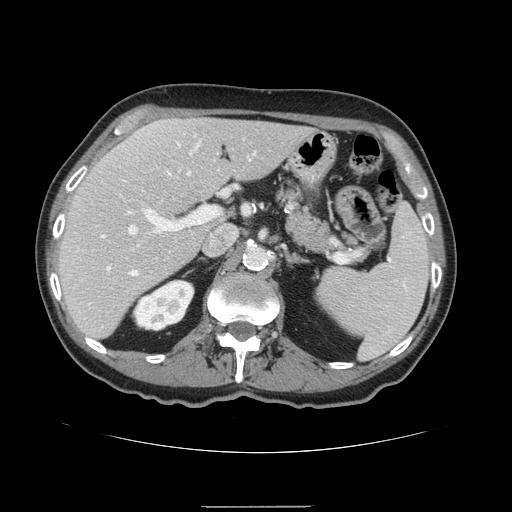
Contrast-enhanced abdominal CT, one axial slice; position 92 of 168 along the scan axis; soft-tissue window (W 400 / L 40 HU); 2.5 mm slice thickness; 512 × 512 image matrix. Male patient, age 74 years. From the clinical record (not read from this slice): diagnosis: colorectal cancer liver metastases, imaged before liver resection; multiple liver metastases: no; largest metastasis: 14.5 cm; chemotherapy before resection: no.
Outlined on this slice (outlined manually by an expert reader):
- hepatic veins: bounding box <128,158,251,274> (left, top, right, bottom; pixels)
- liver: <58,119,313,339>
- planned liver remnant (the part of the liver to remain after resection): <58,119,314,339>
- portal vein (with intrahepatic branches): <76,195,220,271>